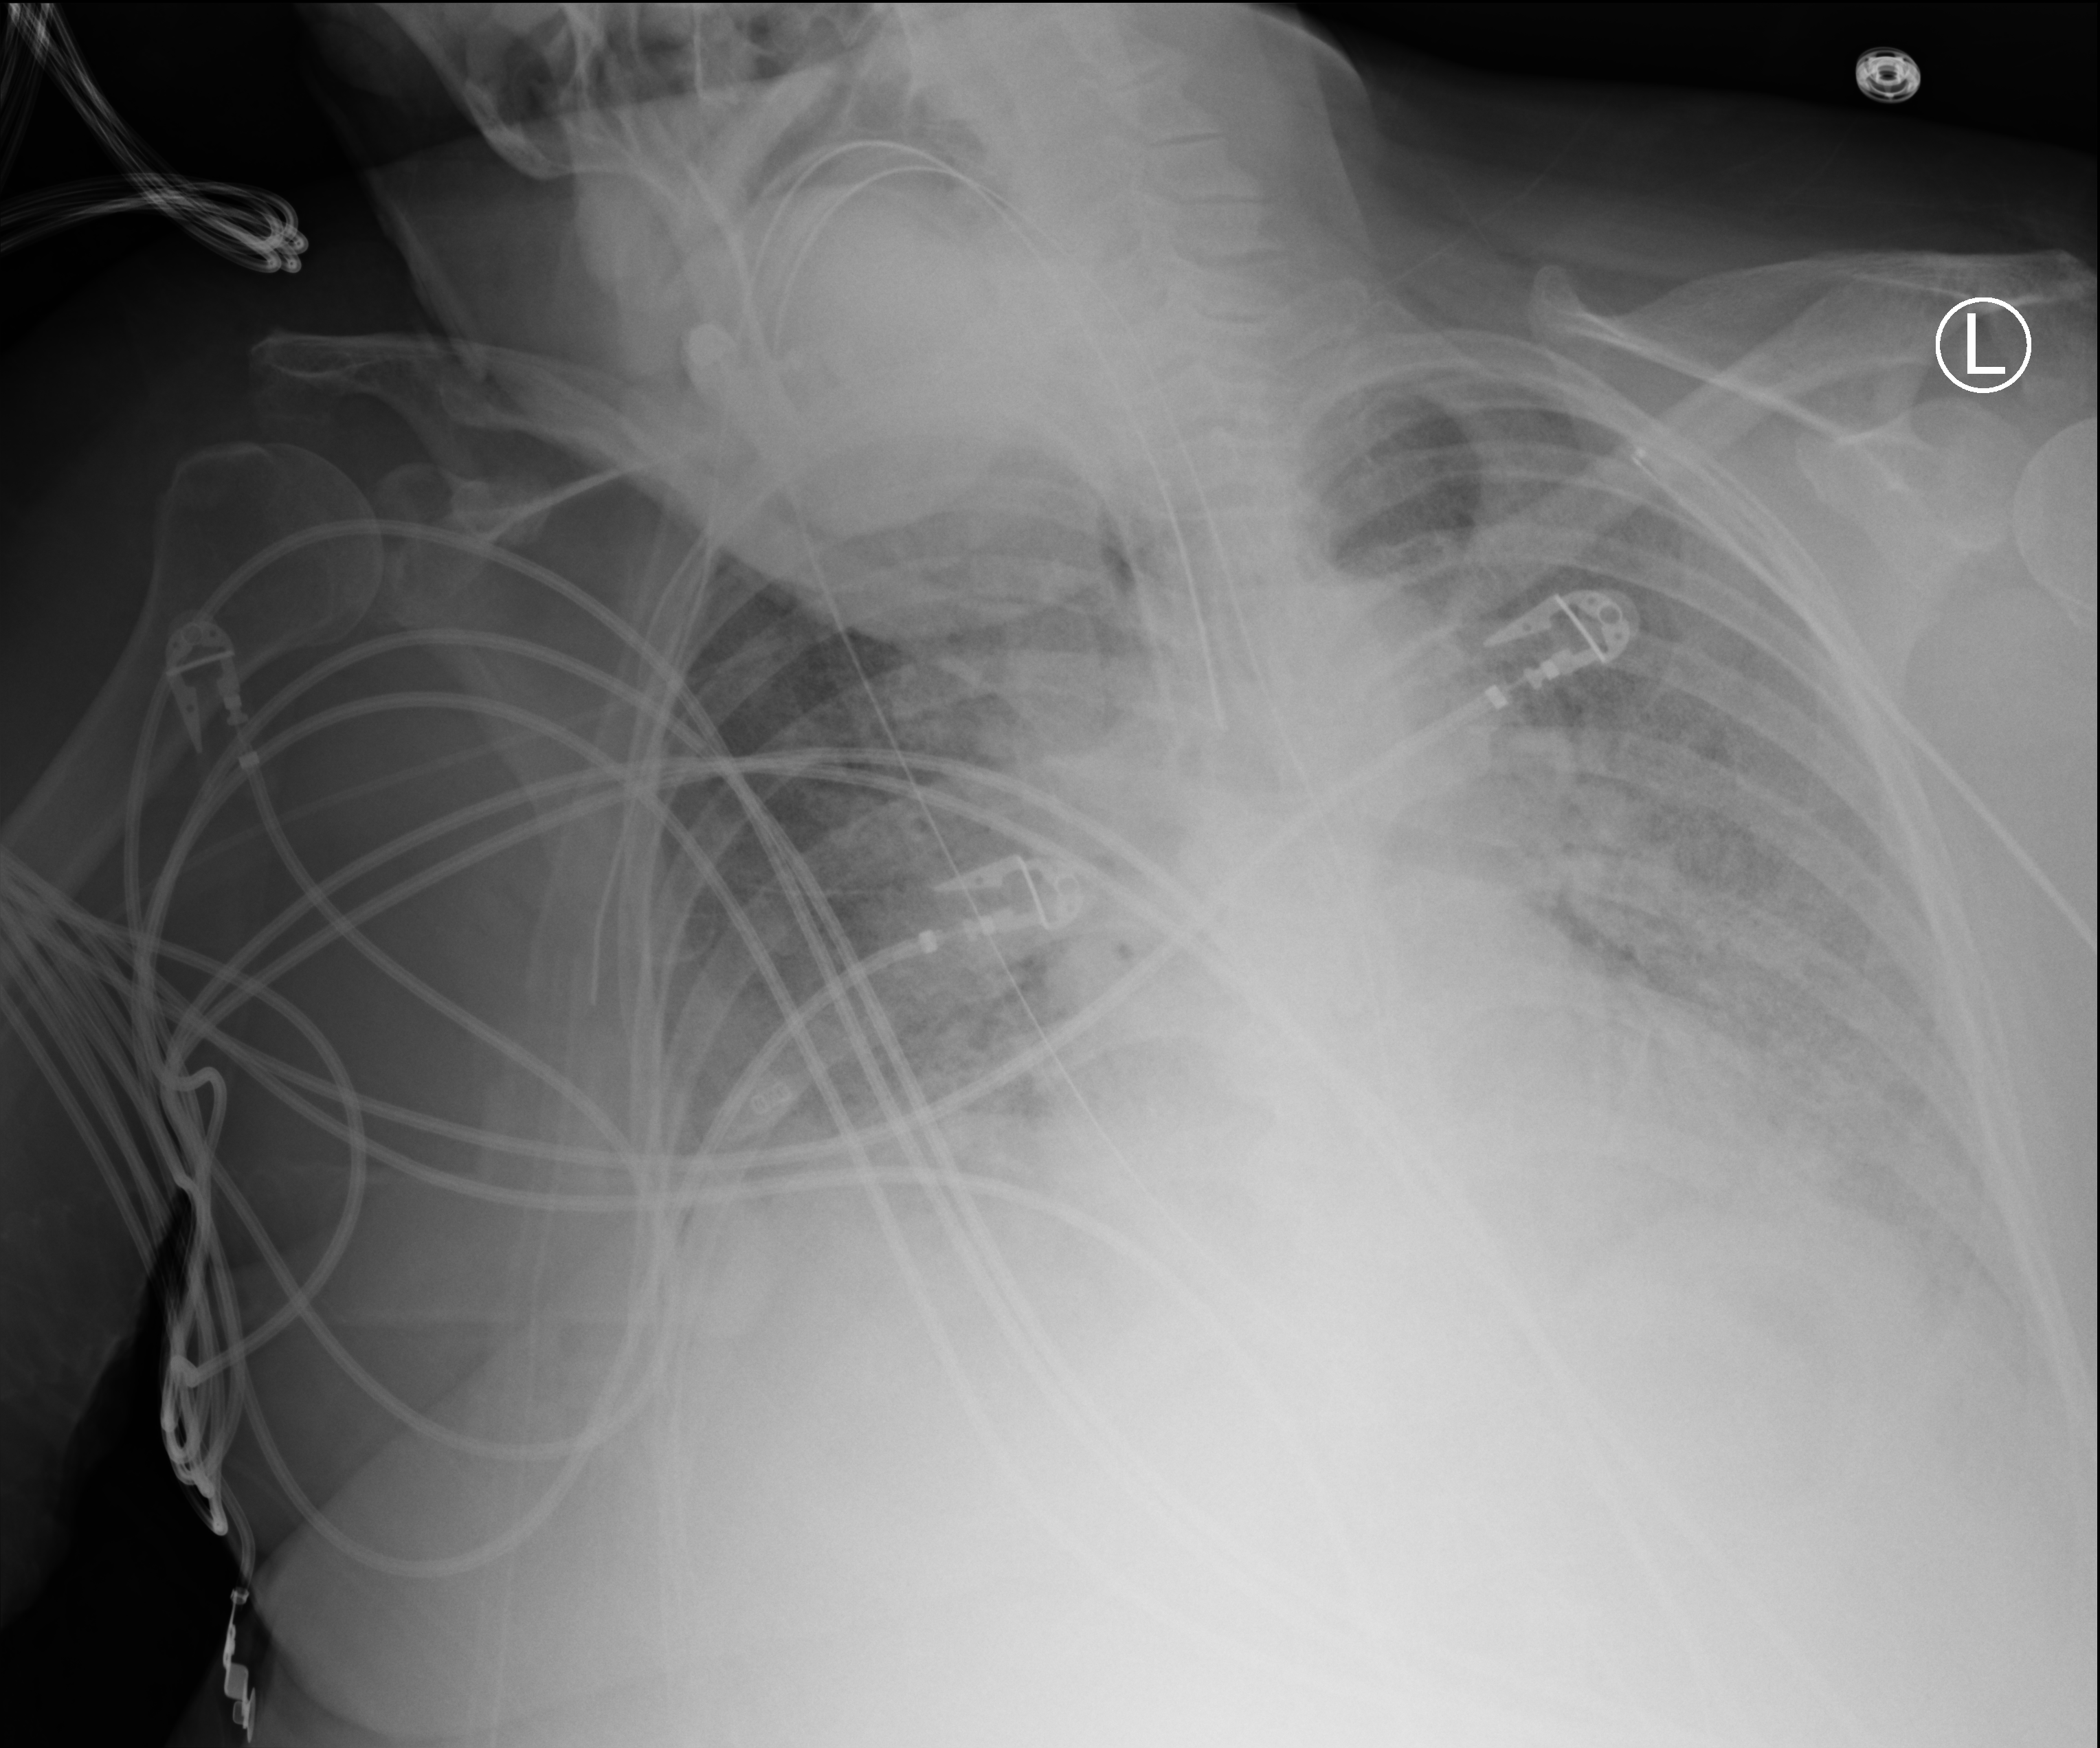
Bedside chest radiograph (computed radiography), anteroposterior (AP) projection. Female patient hospitalised with COVID-19, age 60–74 years.
Admission-level facts for this patient (not findings on this image; timing relative to this image not recorded):
- hypertension (admission record): no
- COPD (admission record): no